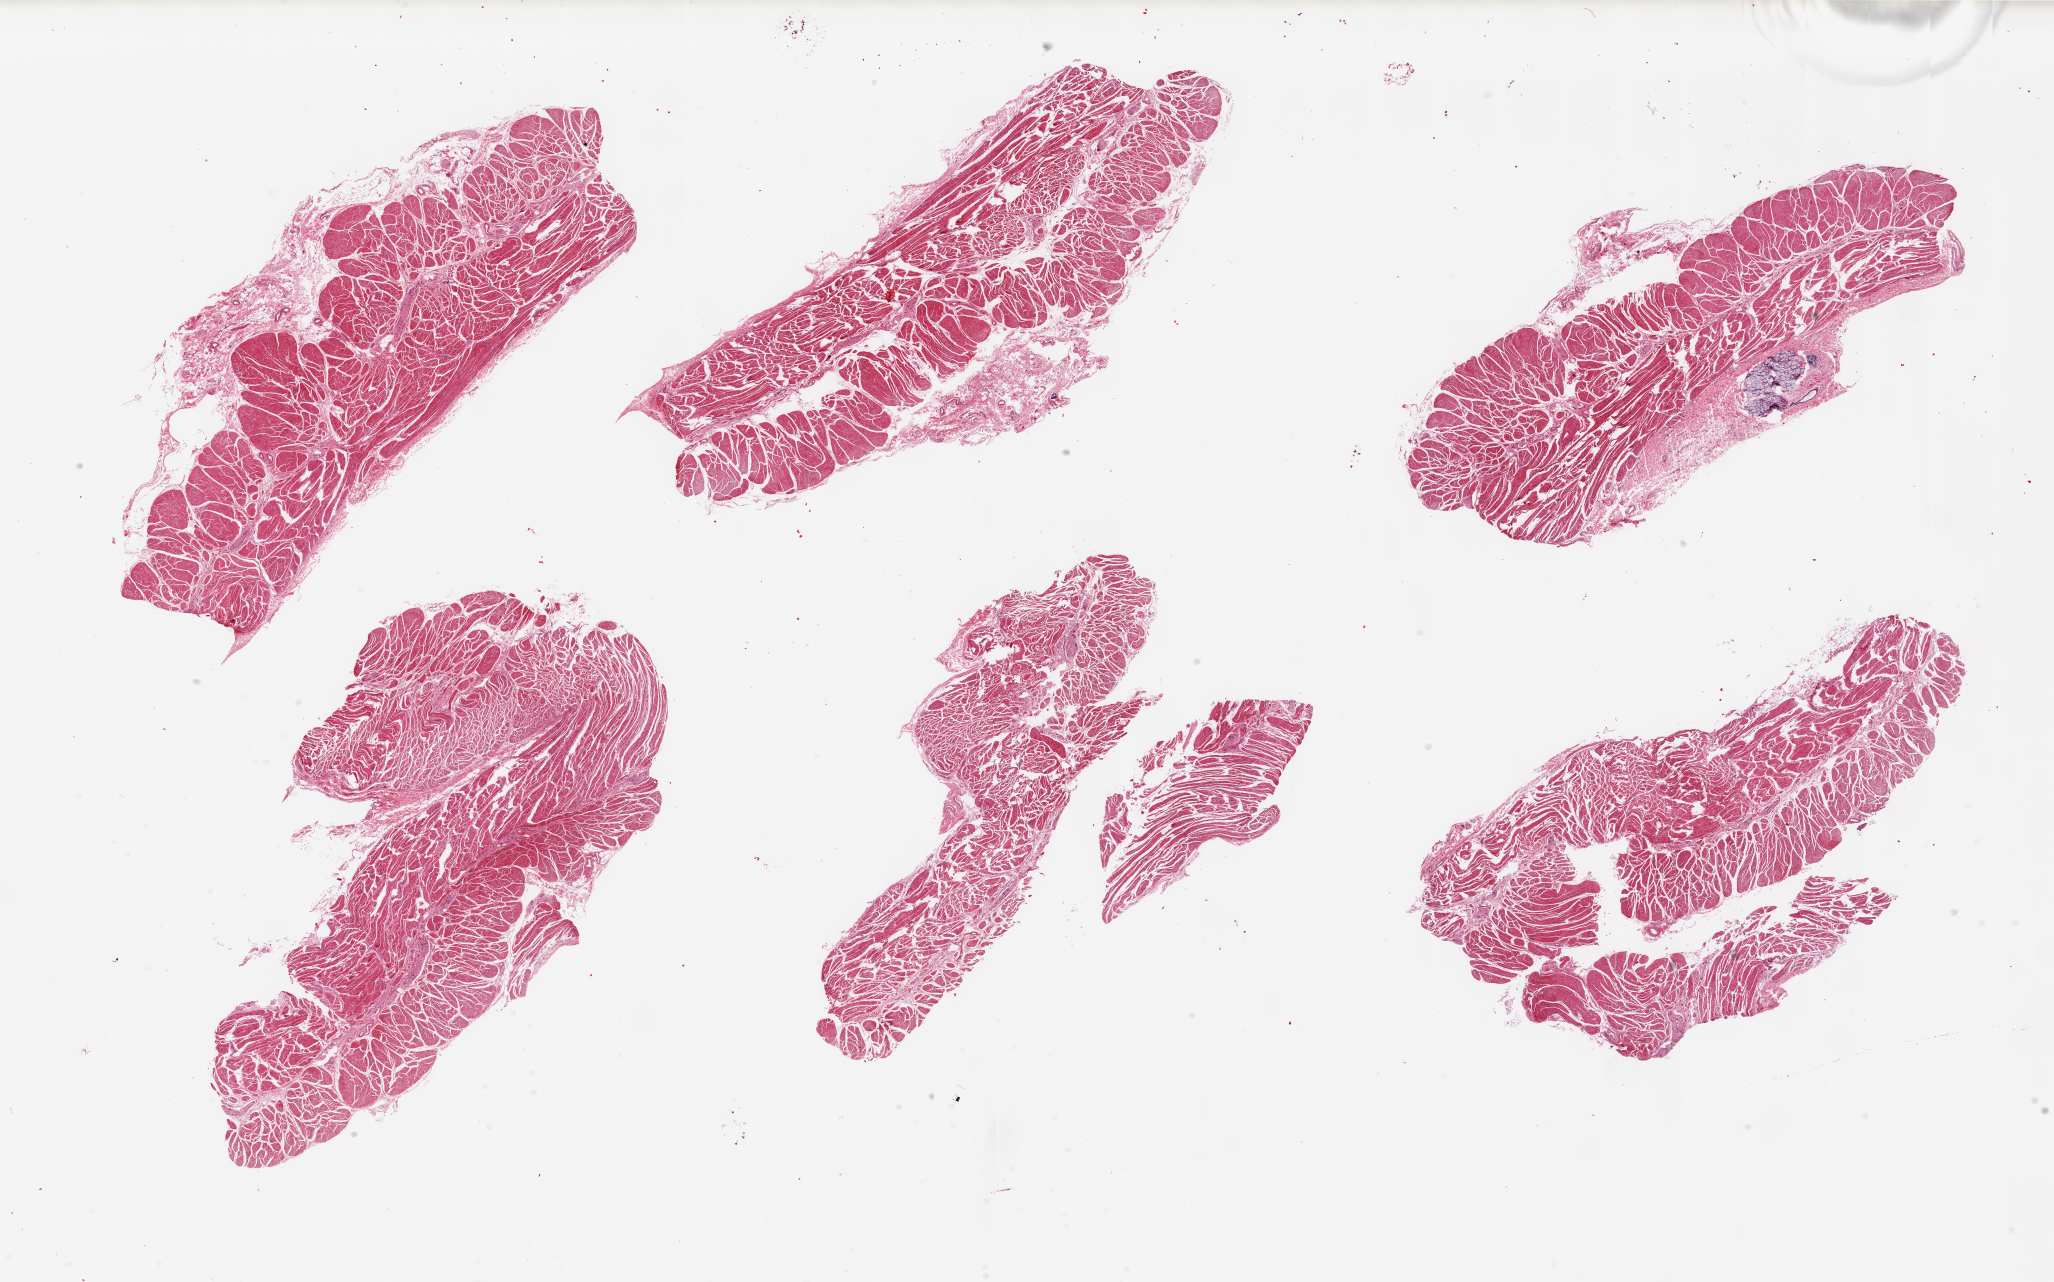
Digitized haematoxylin and eosin-stained section — low-resolution overview of the scanned area, about 32.5 x 20.3 mm (acquisition: 20x scan), PAXgene-fixed, paraffin-embedded tissue, section of gastroesophageal junction (target tissue), tissue donor sample. Donor sex: male.
* review note (as recorded): 6 pieces, confirmed target muscularis, trace mucus glands